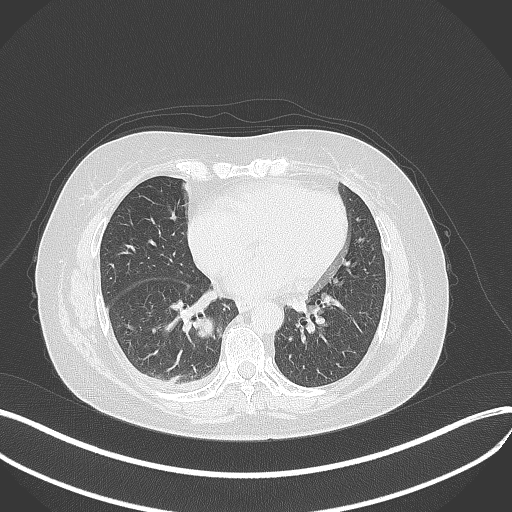
Chest CT, one axial slice. Reconstruction kernel B70f. 120 kVp. Lung window (W 1500 / L -600 HU). 512 × 512 image matrix, field of view 400 × 400 mm. Patient: female, 56 years. Case-level facts recorded for this patient, not image findings: clinical TNM (as recorded): T2b N1 M0; histopathological grade: G3.
Structures marked on this image (rectangle marked by the reading radiologist):
- lung tumour (recorded histology: small cell carcinoma): bounding box <190,310,215,343> (left, top, right, bottom; pixels)